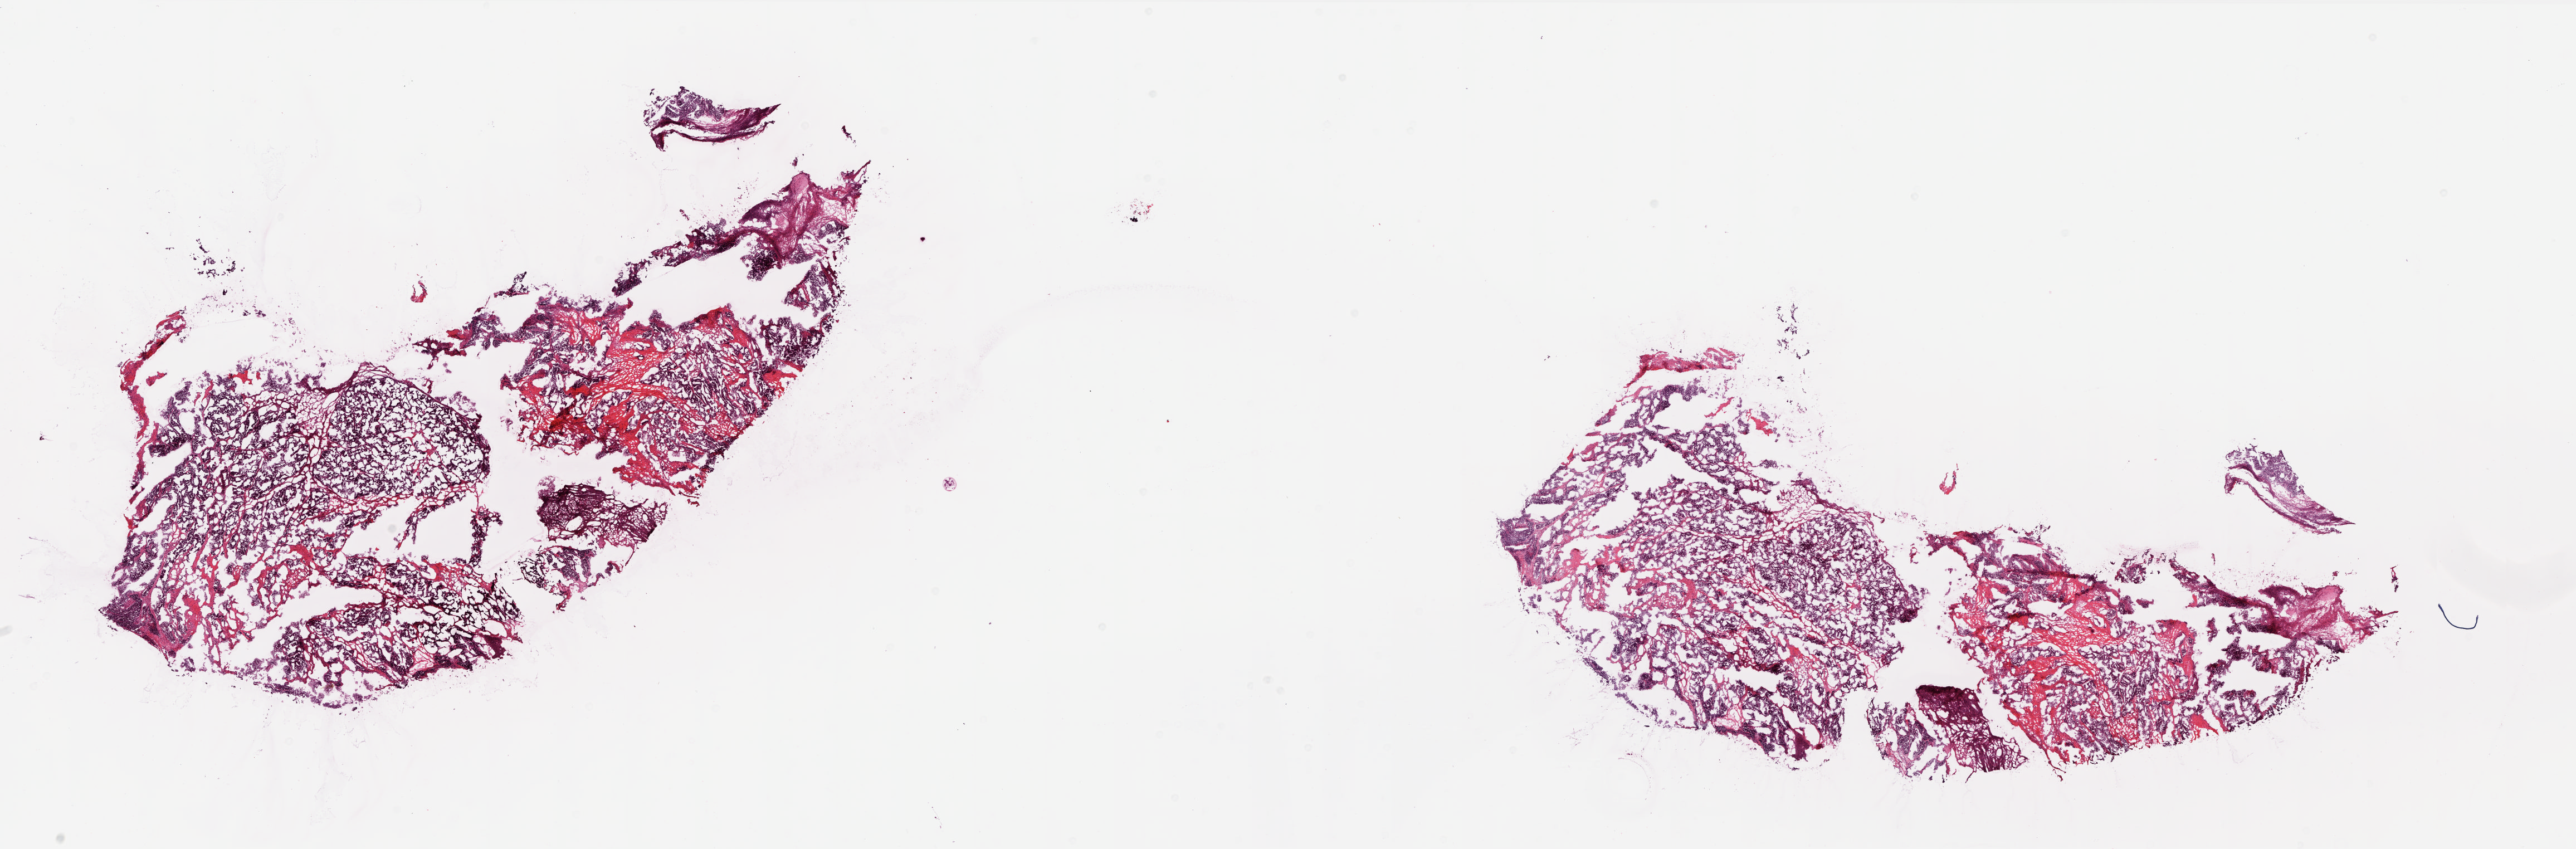
Digitized Hematoxylin and eosin (H&E) stained tissue section (whole slide) — low-resolution overview of the scanned area, about 36.9 x 12.2 mm (acquisition: 20x scan), frozen section from the top of the tissue portion, ovary, primary tumour sample. Patient: female, age at initial diagnosis 60 years. Histologic grade: G2 (moderately differentiated). Slide review estimates, as recorded: tumour cells 70%, tumour nuclei 90%, normal cells 0%, stromal cells 15%, necrosis 15%.
FIGO stage: IB. Pathologic diagnosis: Serous cystadenocarcinoma, NOS.